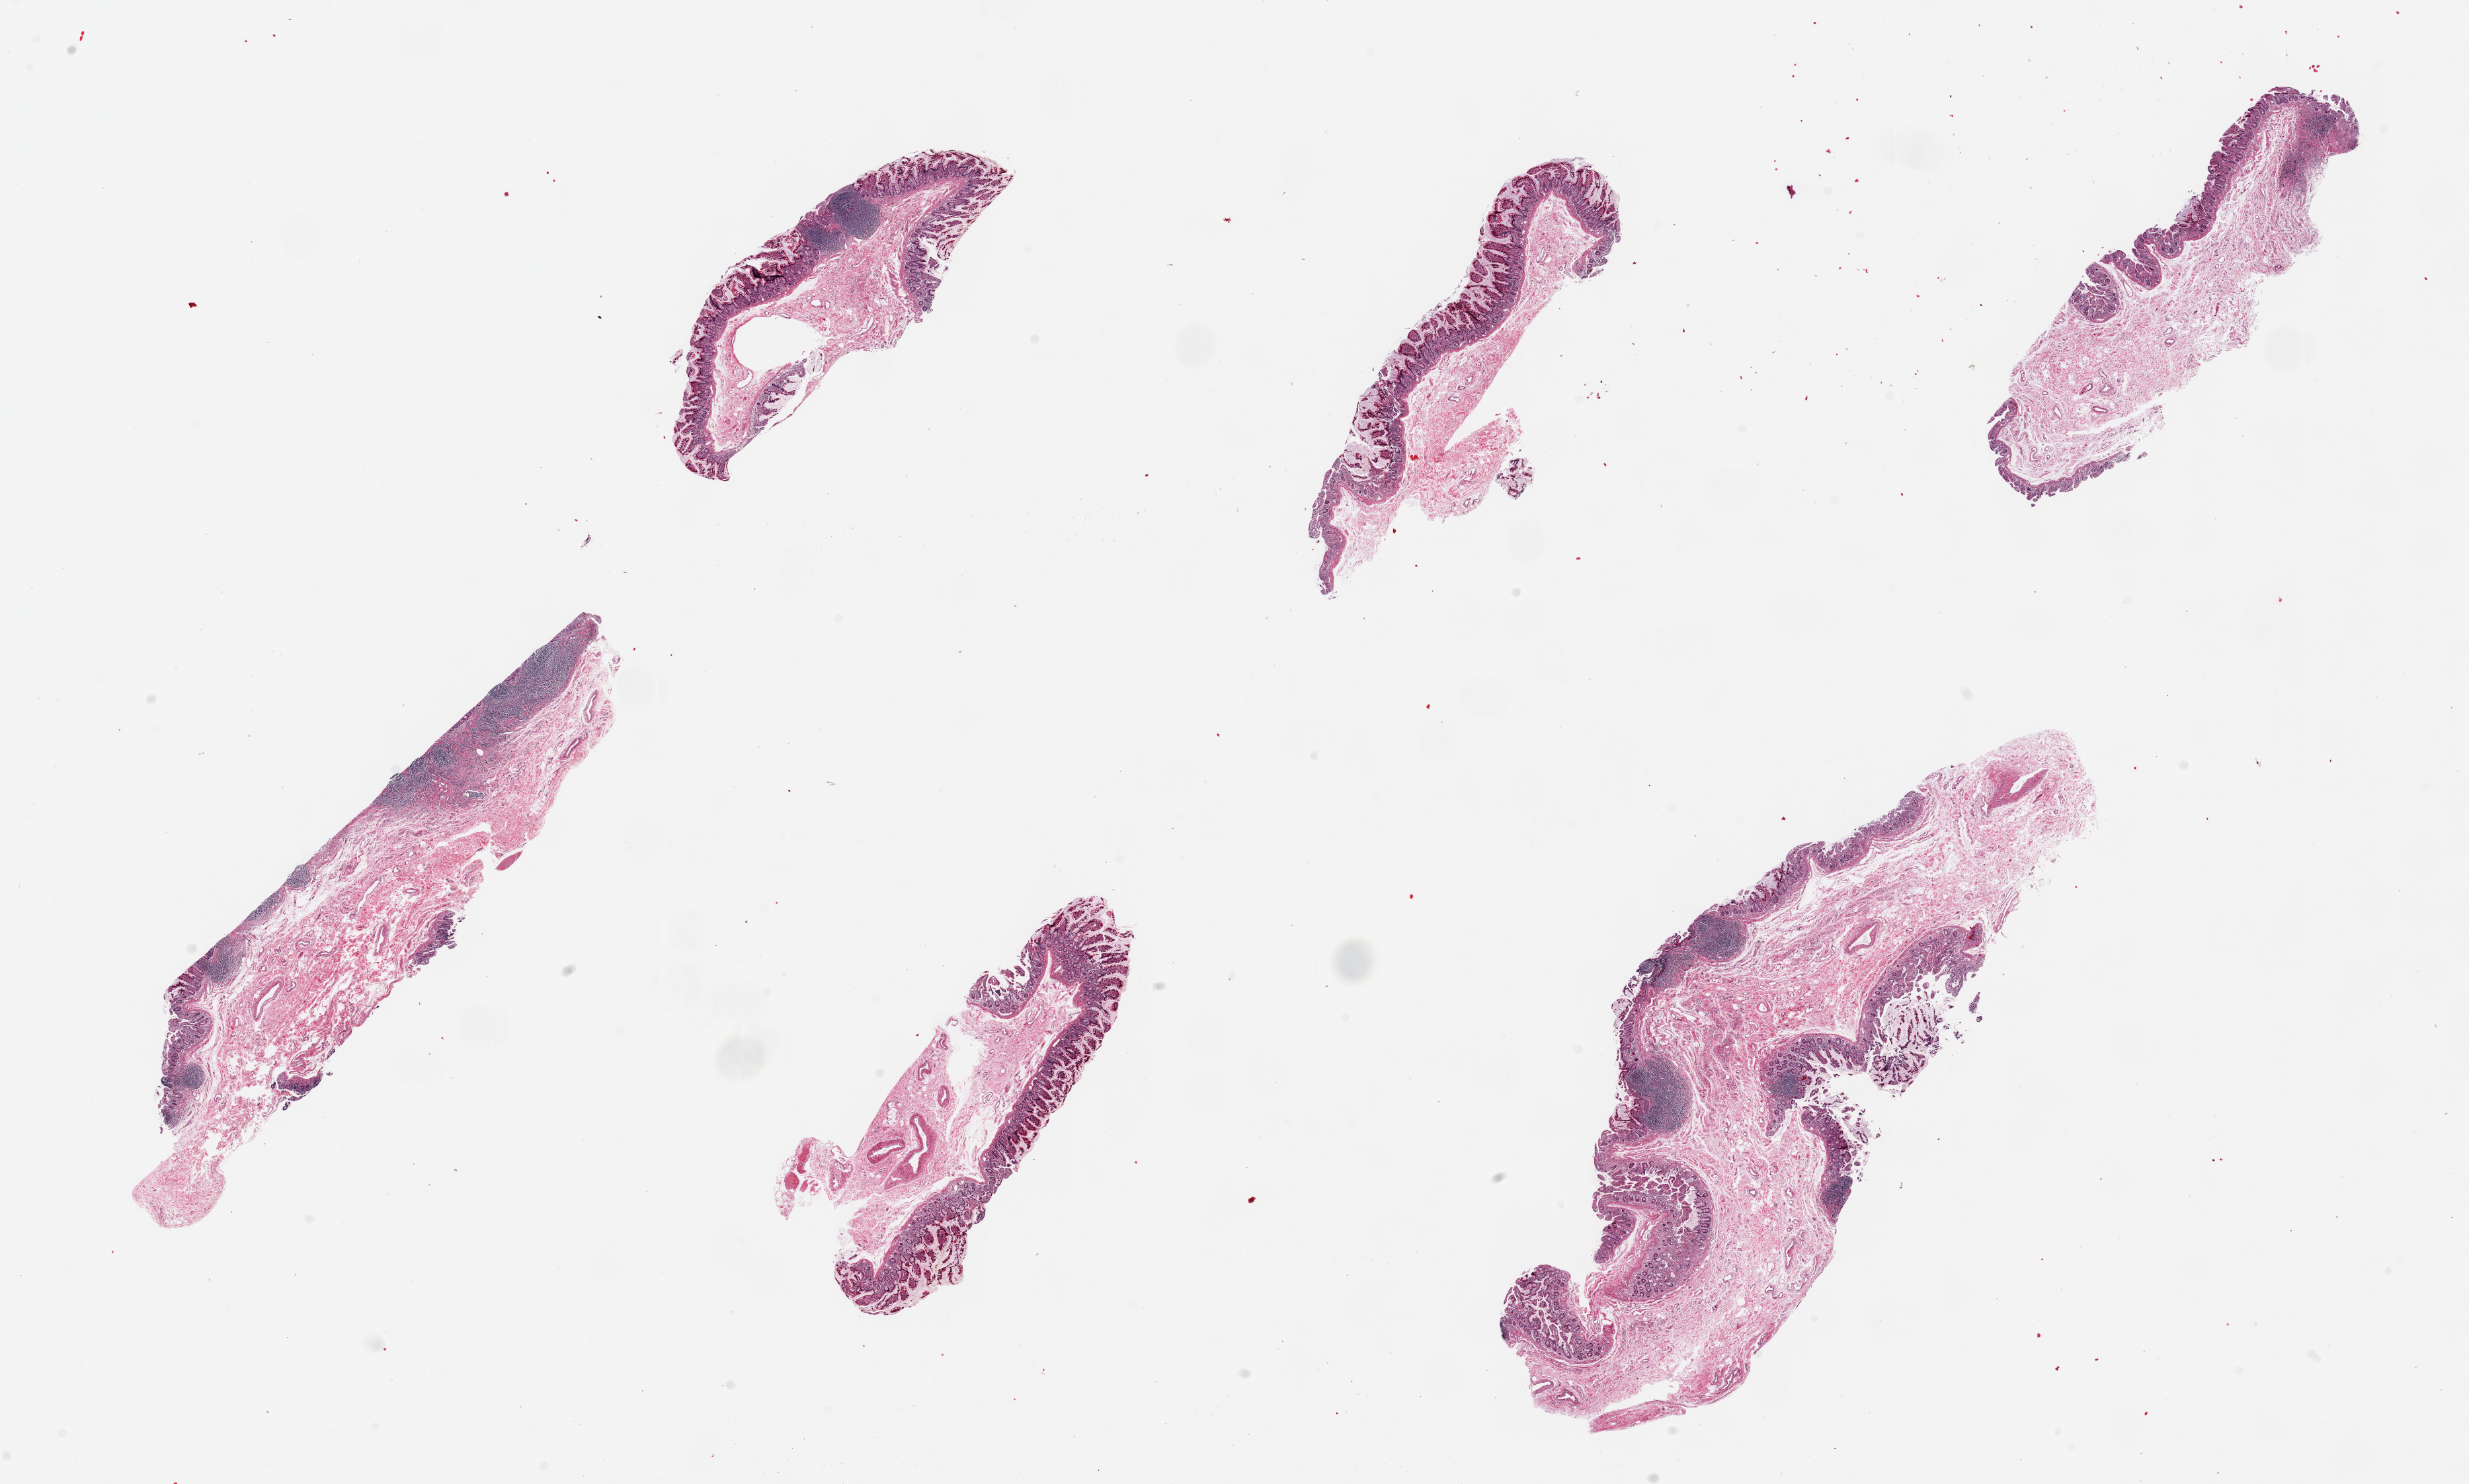
Whole-slide image, hematoxylin and eosin (H&E) stain — a low-resolution overview of the entire scanned area, about 29.5 x 17.8 mm (from a 20x scan); PAXgene-fixed paraffin-embedded (PFPE) section; target tissue: ileum; donor tissue sample. Donor sex: male.
Review note (as recorded): 6 pieces, up to 10x4mm; good specimens, all mucosa, ~10% Peyer patches.